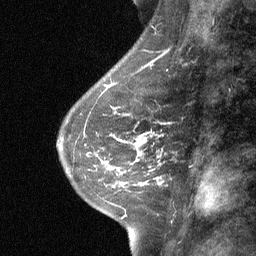
Breast MRI (dynamic contrast-enhanced), one sagittal slice. Slice 26 of 64 in the series (ordered by position). Dynamic contrast-enhanced study with each time point stored as its own series, time point 2 of 3 at this slice position (early post-contrast, ordered by acquisition time). 1.5 T. TE 4.8 ms, TR 27 ms. 2 mm slice thickness. 256 × 256 image matrix, field of view 180 × 180 mm. Patient: female, 42 years. Case-level facts recorded for this patient, not image findings: setting: breast cancer imaged before/during neoadjuvant chemotherapy; receptor status: triple-negative.
Structures marked on this image (semi-automatically segmented with operator editing):
- analysis volume of interest (the breast-tissue region the enhancement analysis was run in; not a lesion): bounding box (x1, y1, x2, y2) in pixels: (99, 117, 174, 187)
- tumour enhancement mask (voxels above the 90 % enhancement threshold inside the analysis volume of interest): (136, 134, 158, 184)